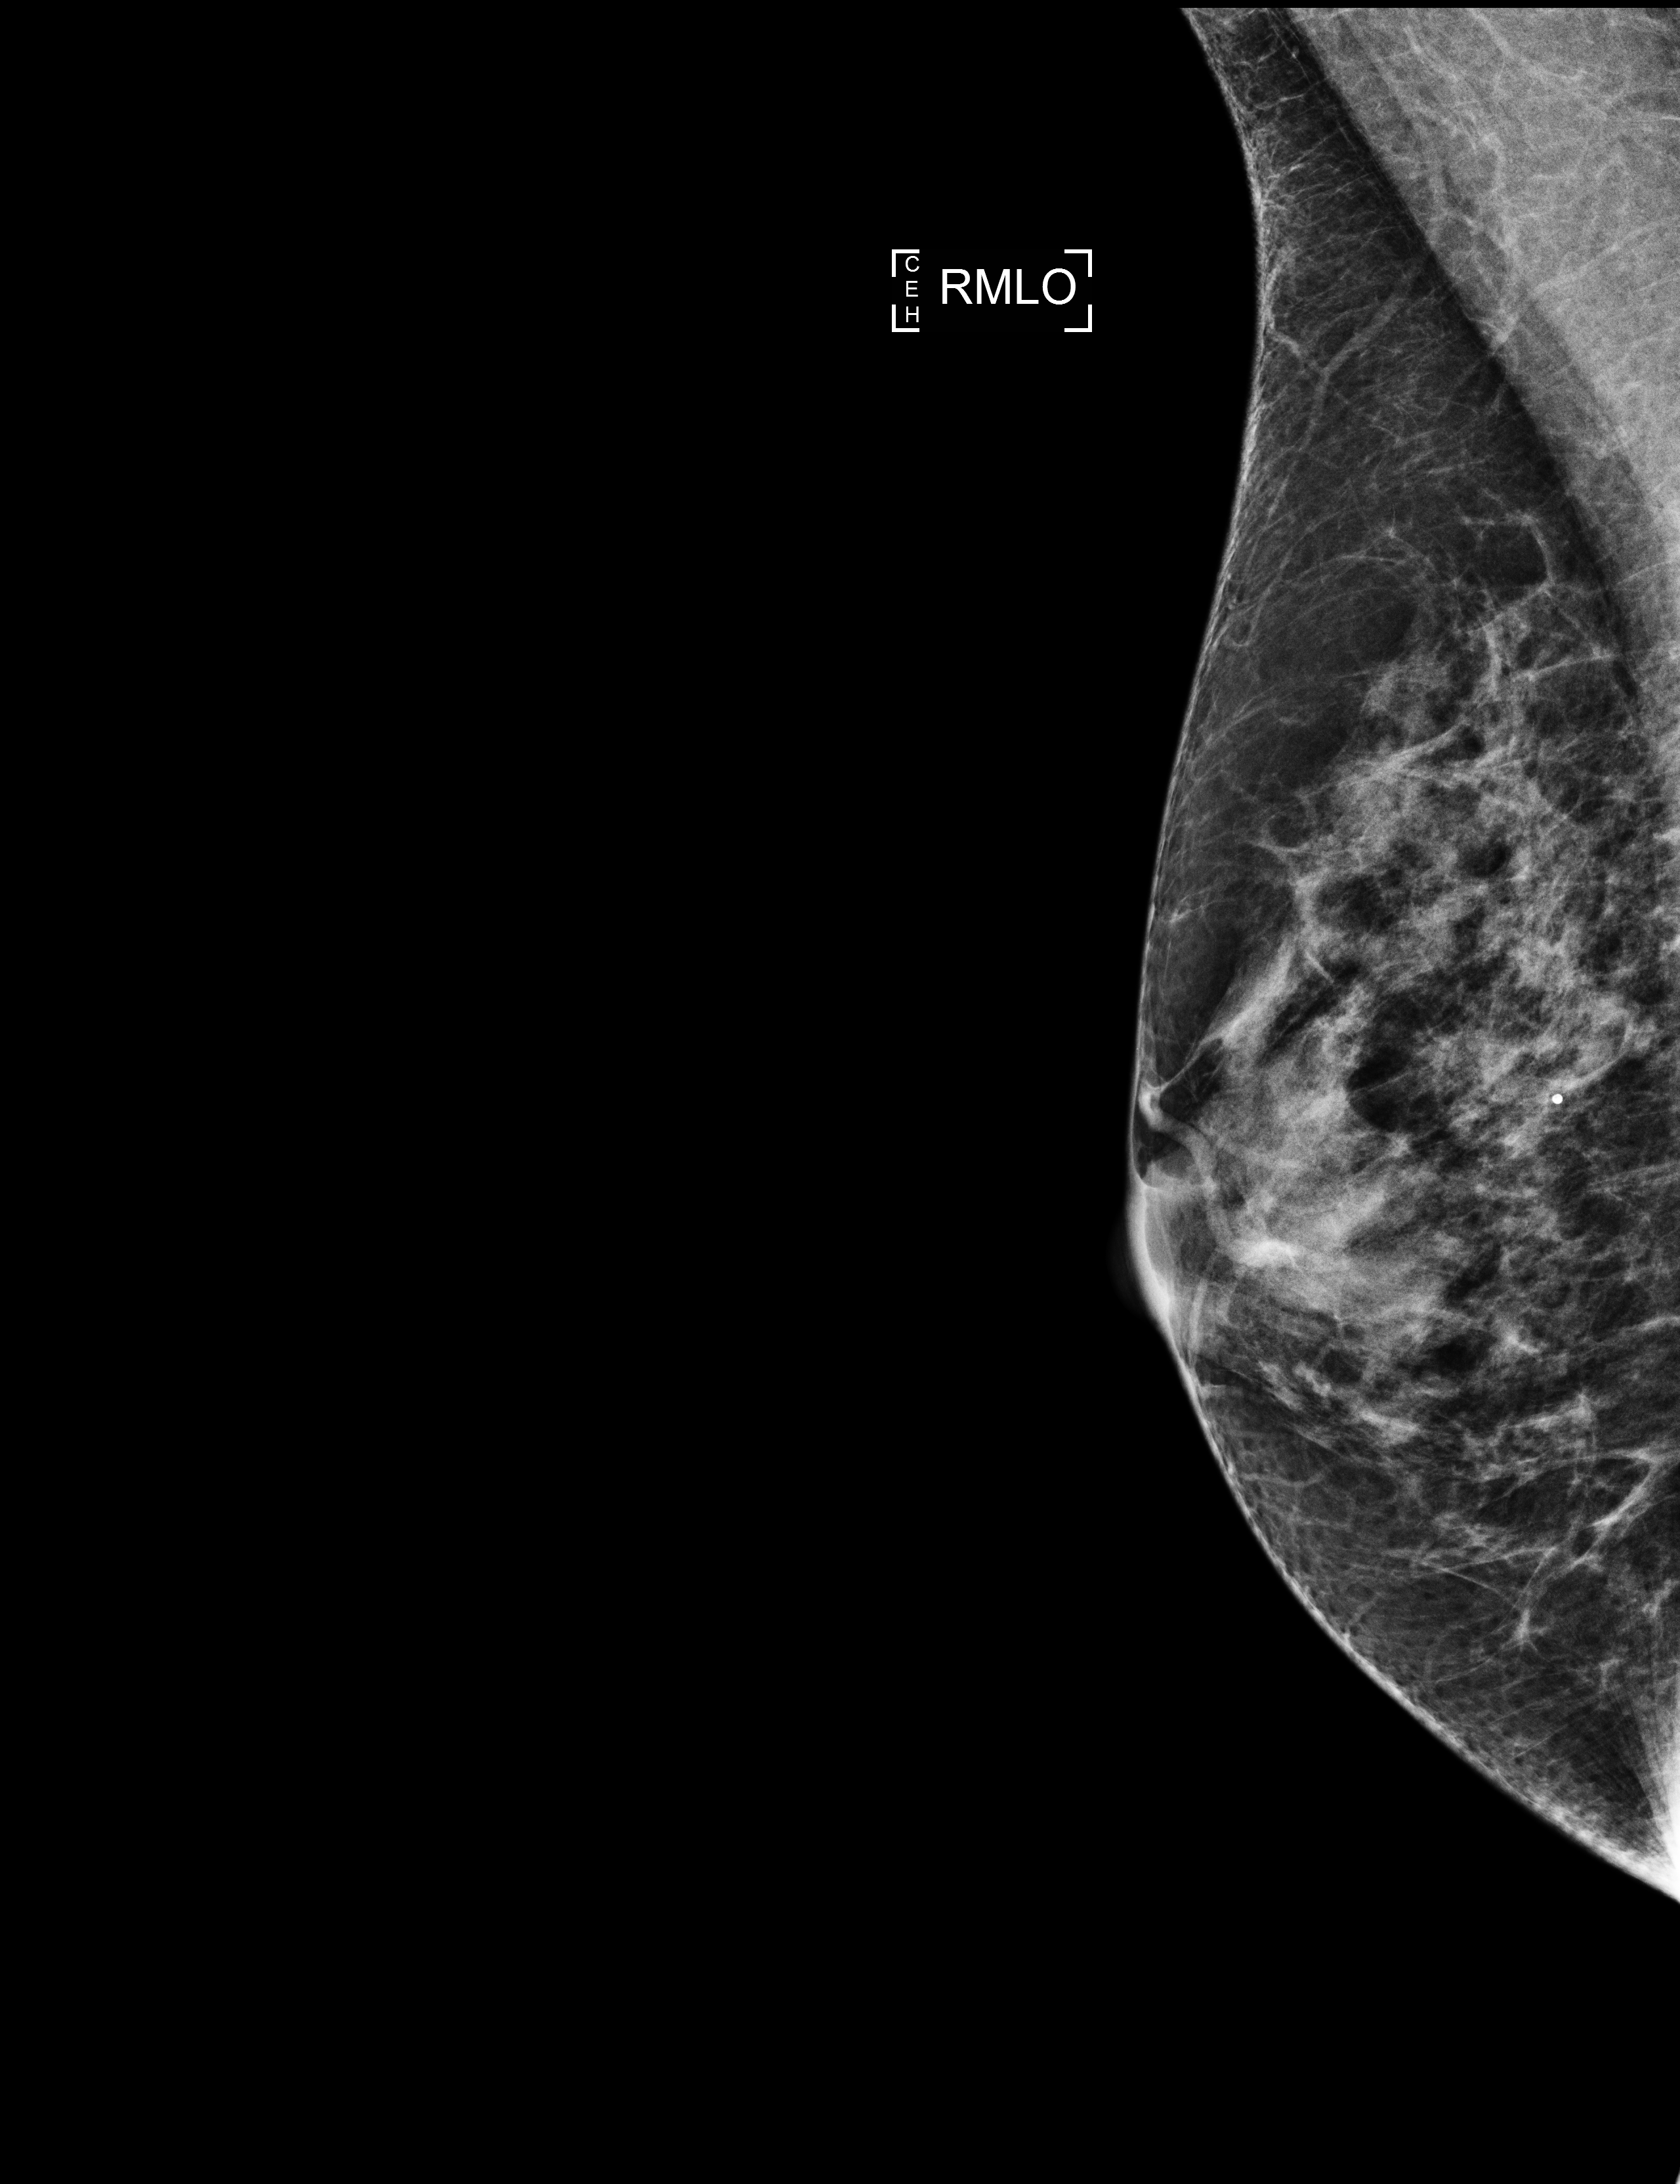
Screening examination, system: Selenia Dimensions. Patient: female, 60 years.
Image type: full-field digital mammogram. Breast: right. Projection: mediolateral oblique (MLO) view.